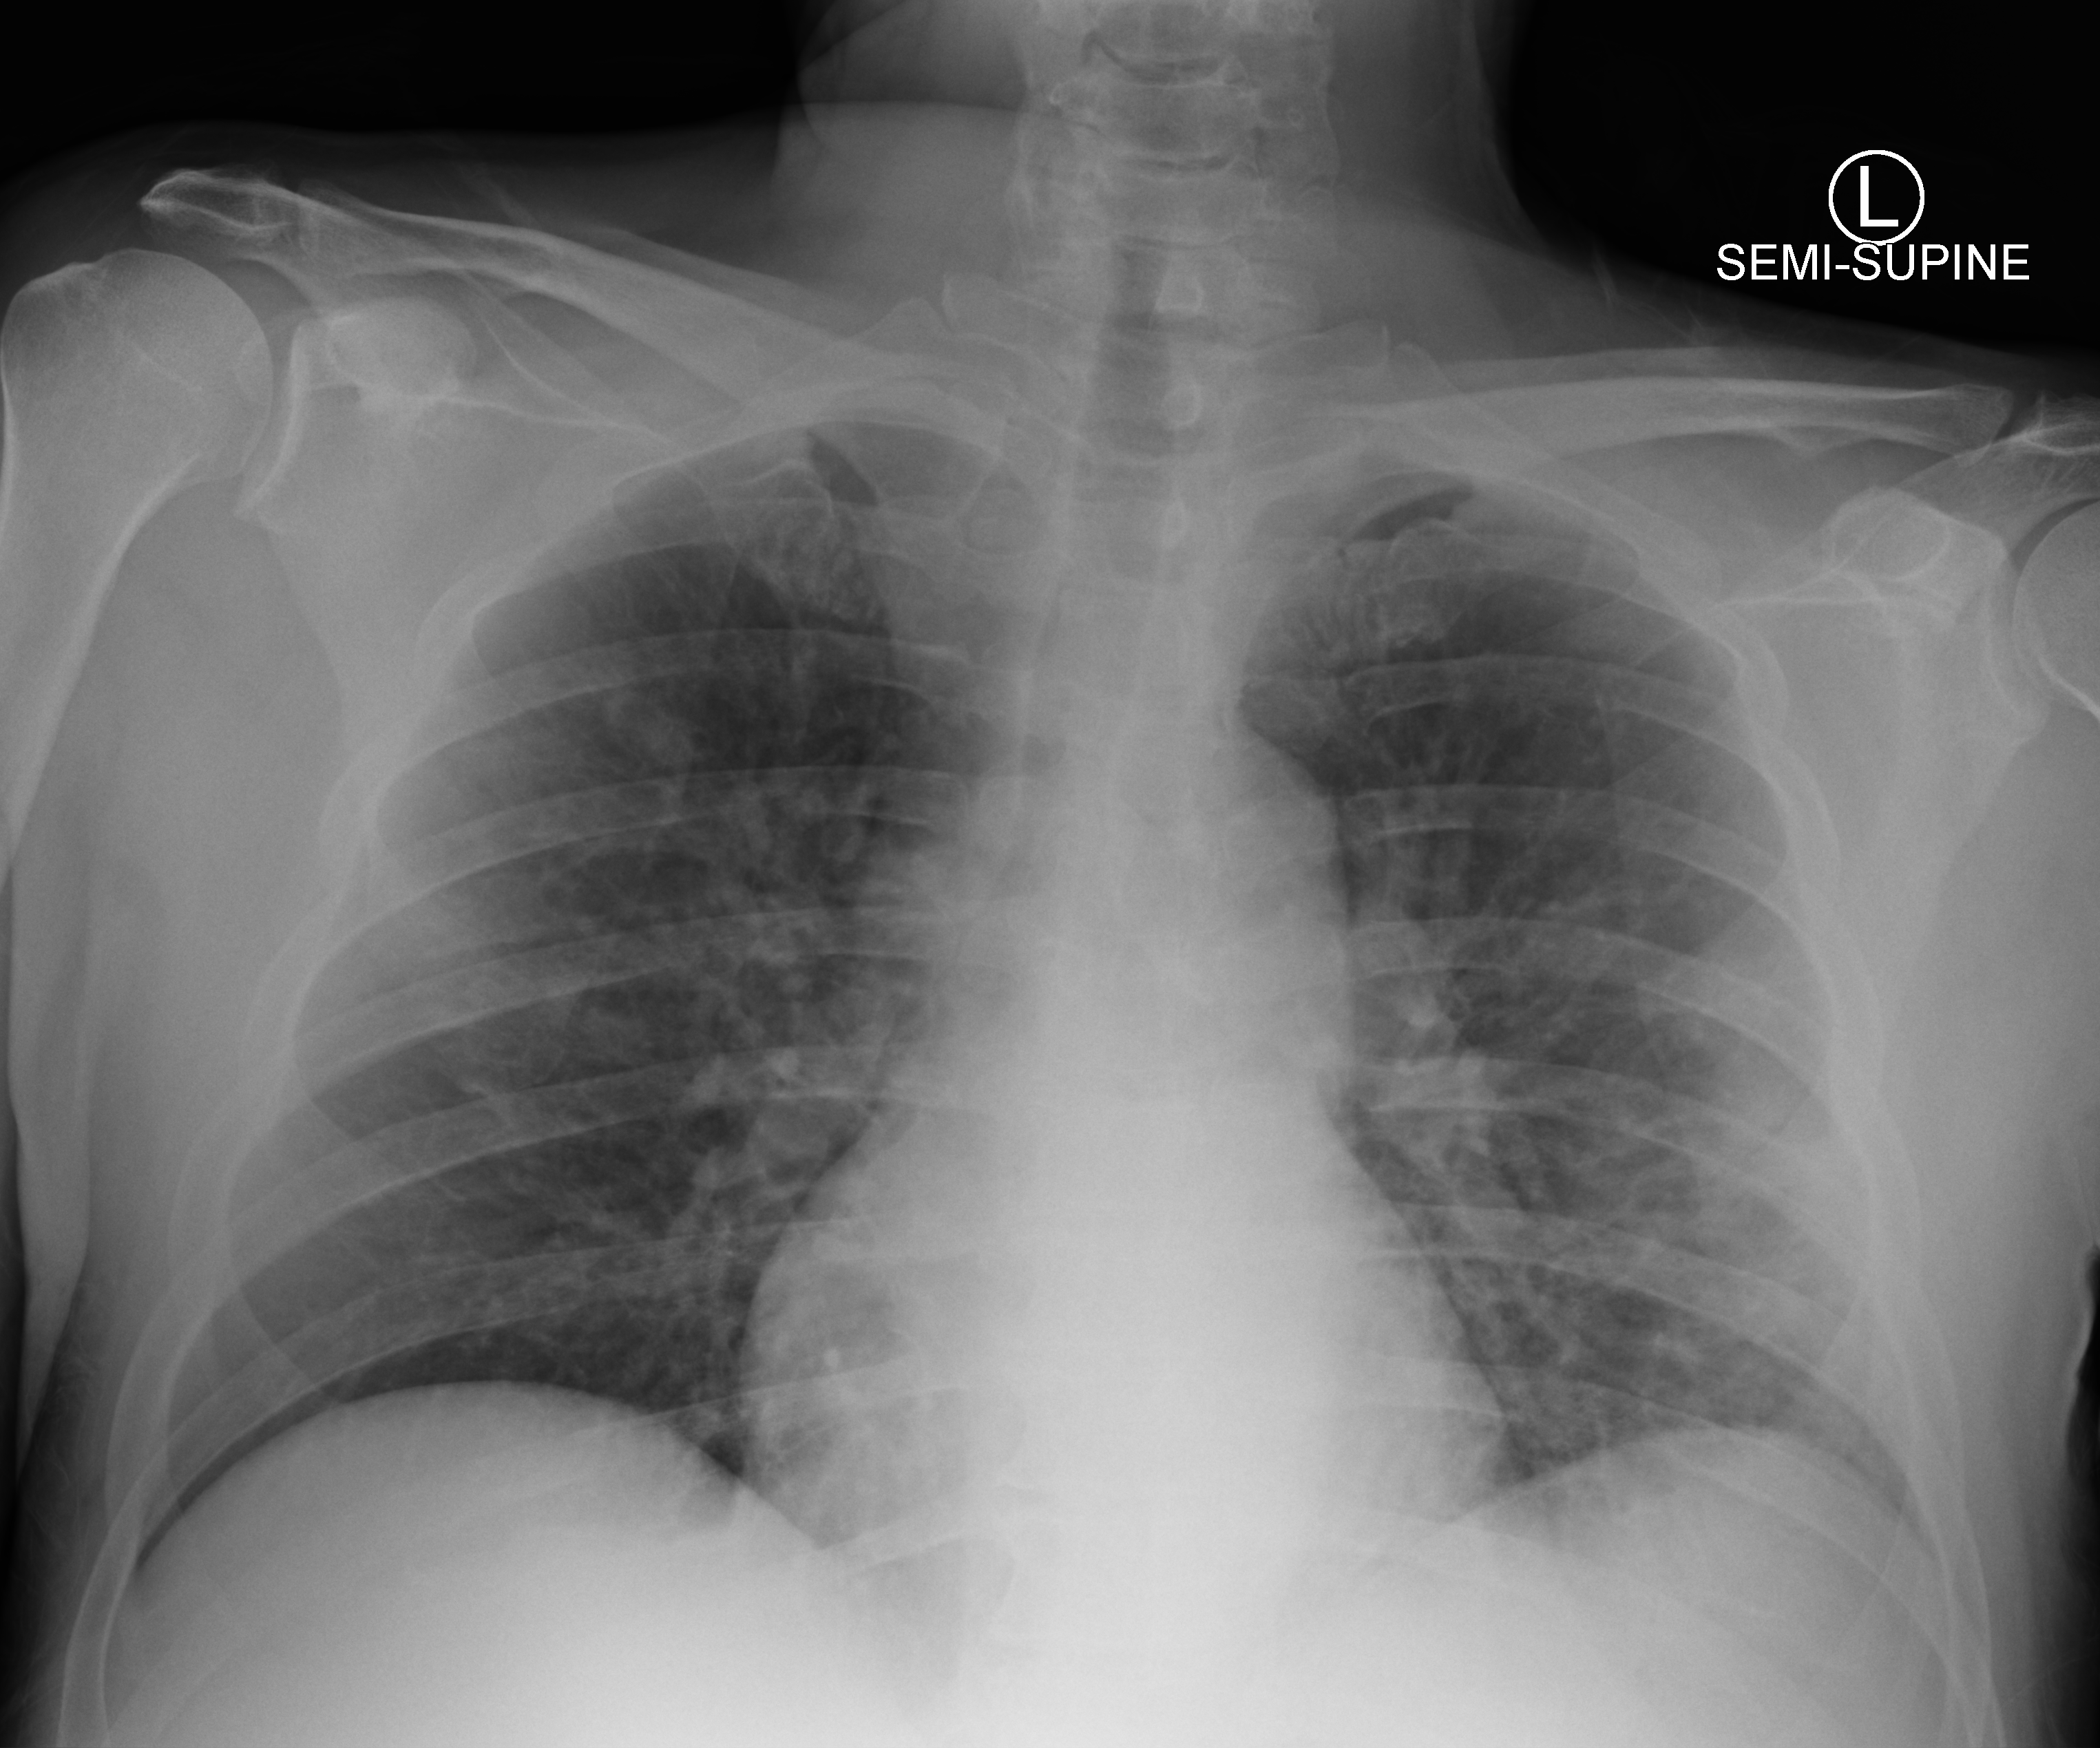
Bedside chest radiograph (computed radiography); anteroposterior (AP) projection. Patient hospitalised with COVID-19; male, aged 18–59 years.
From the hospital-stay record, not from the radiograph (when in the stay this image was taken is not recorded): chronic kidney disease (admission record): no.